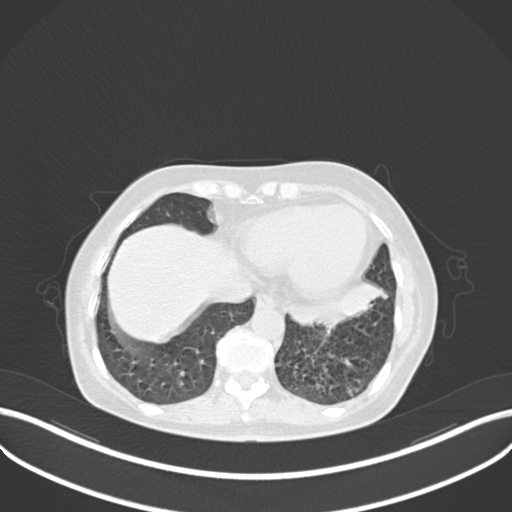
Chest CT, one axial slice; position 64 of 270 along the scan axis; 120 kVp; lung window (W 1500 / L -600 HU); 1 mm slice thickness; 512 × 512 image matrix. Patient: female, 63 years. Case-level facts recorded for this patient, not image findings: clinical TNM (as recorded): T1b N0 M0; histopathological grade: G2-3.
Outlined on this slice (rectangle marked by the reading radiologist):
- lung tumour (recorded histology: adenocarcinoma): bounding box <282,275,386,331> (left, top, right, bottom; pixels)